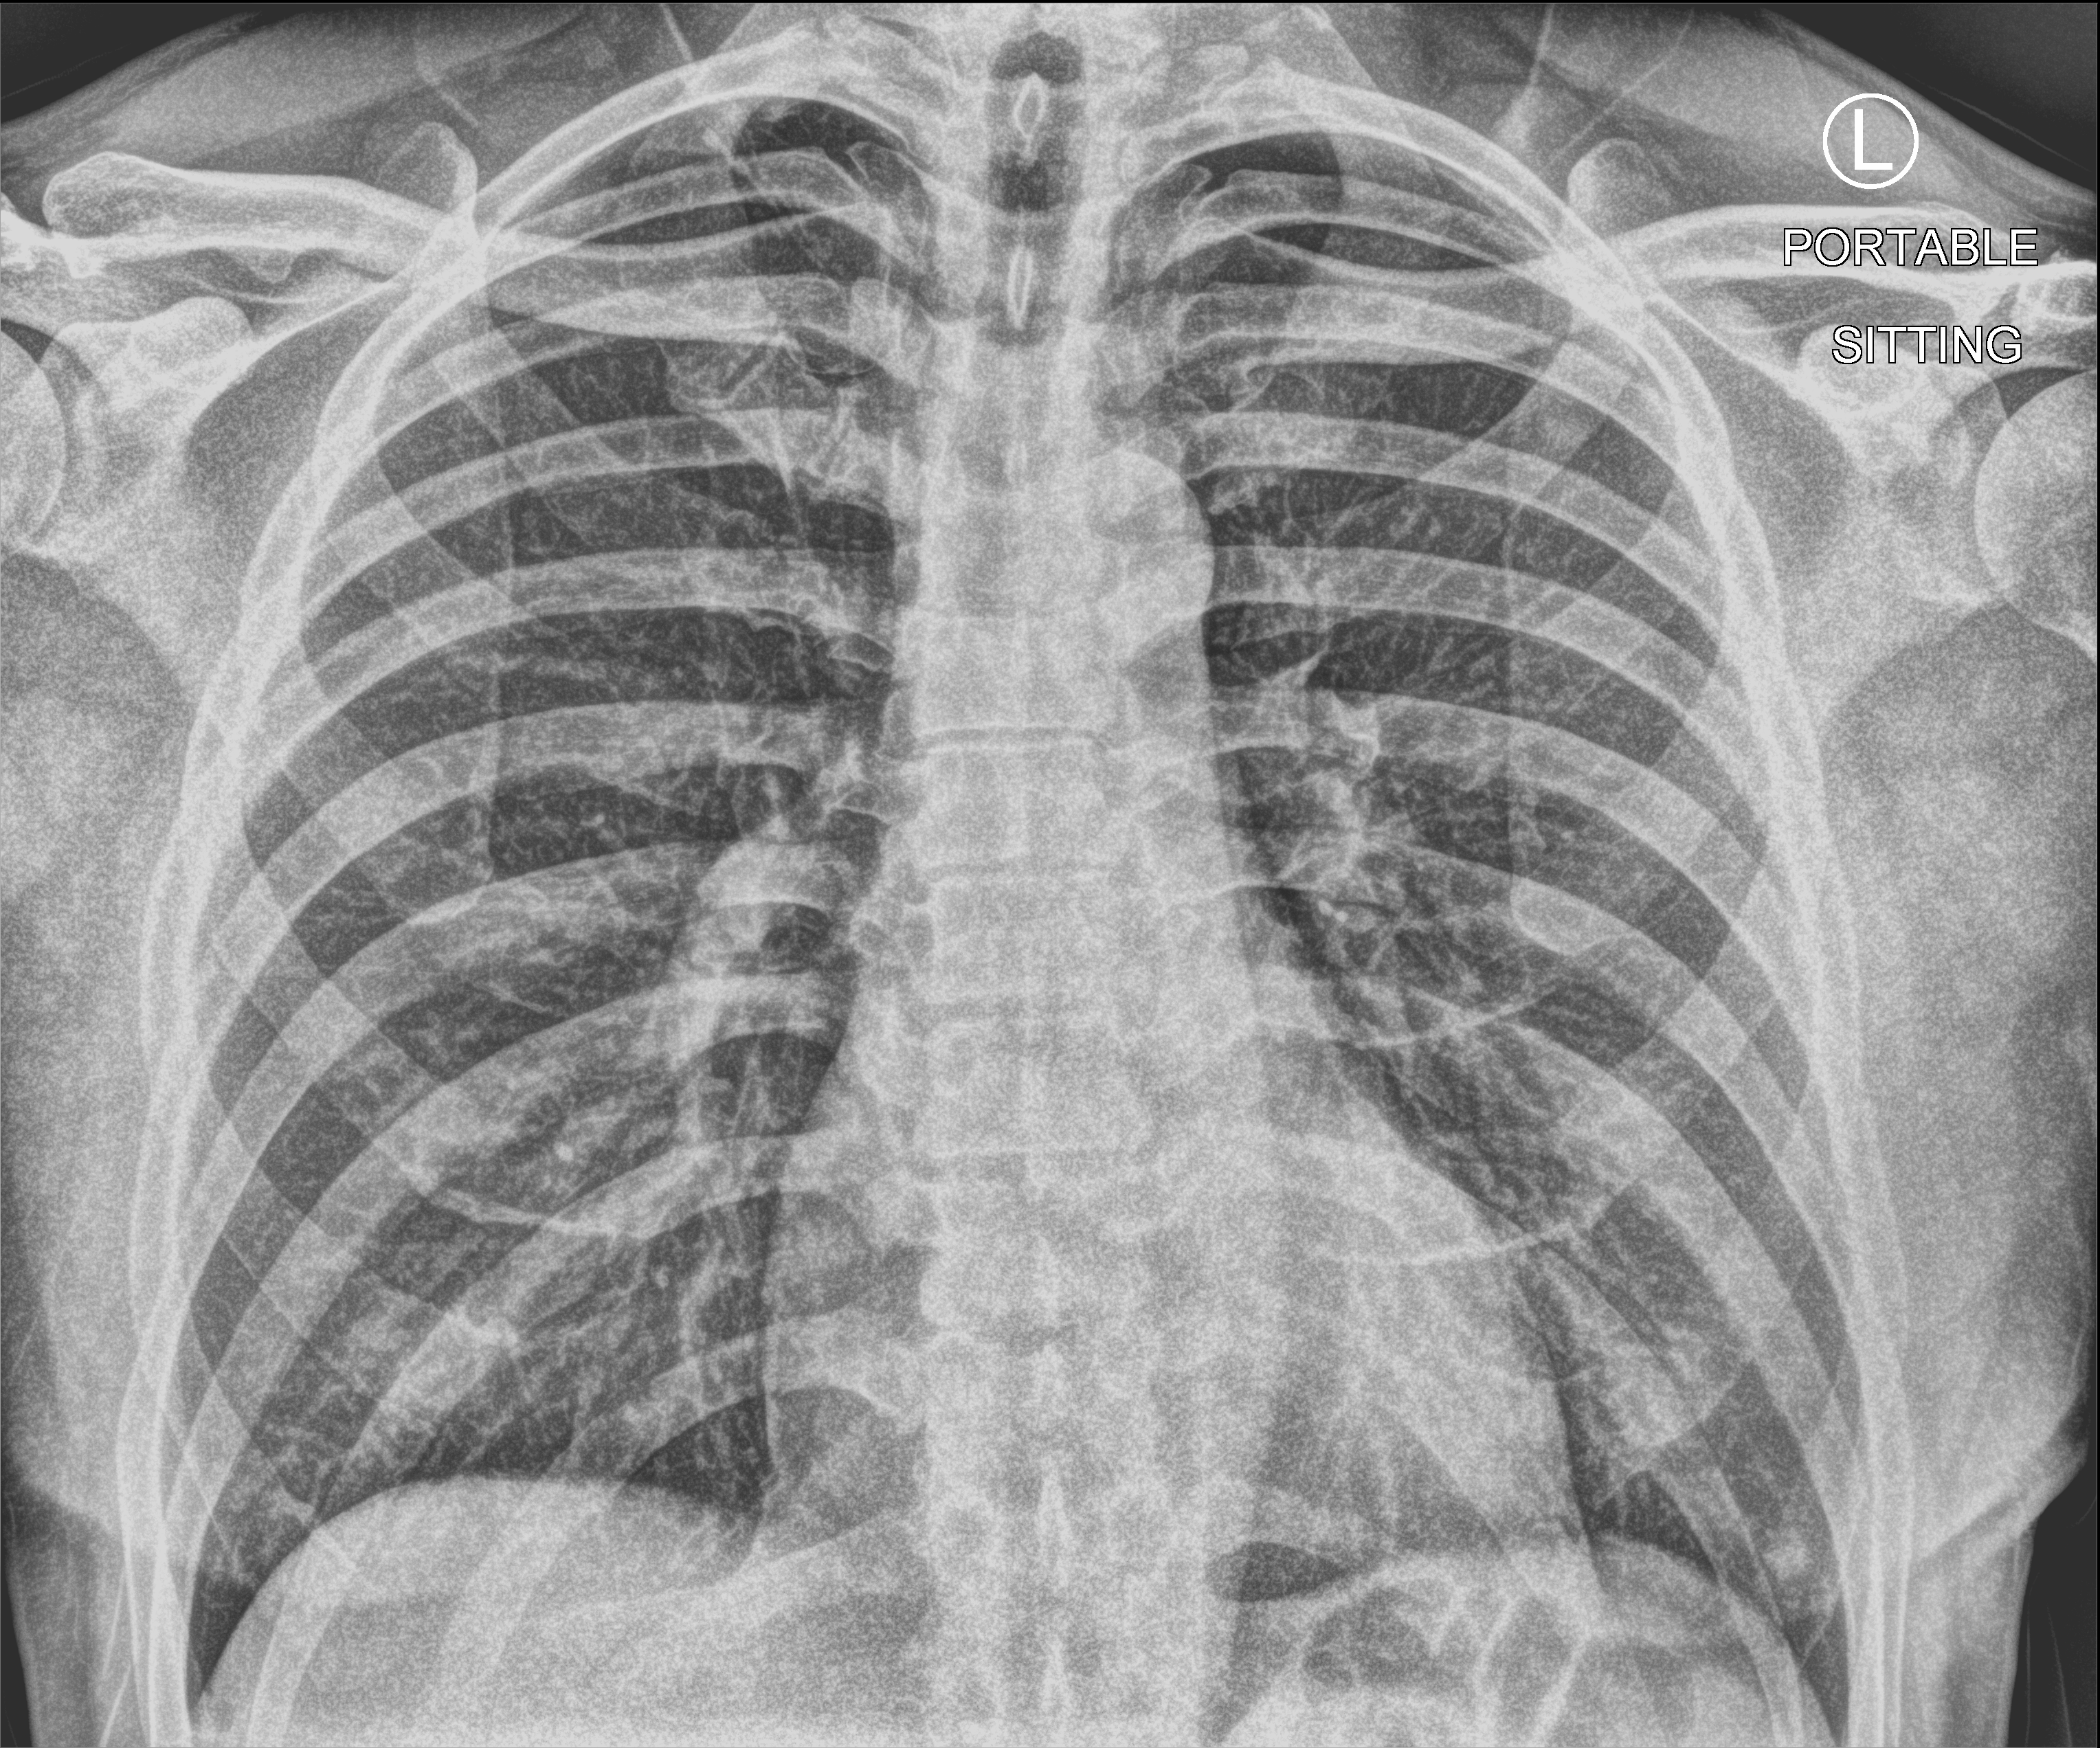
Chest X-ray (portable), anteroposterior (AP) projection. Male patient hospitalised with COVID-19, age 18–59 years.
Admission-level facts for this patient (not findings on this image; timing relative to this image not recorded):
- length of hospital stay: 1 day
- mechanically ventilated during this hospital stay: no
- admitted to intensive care during this hospital stay: no